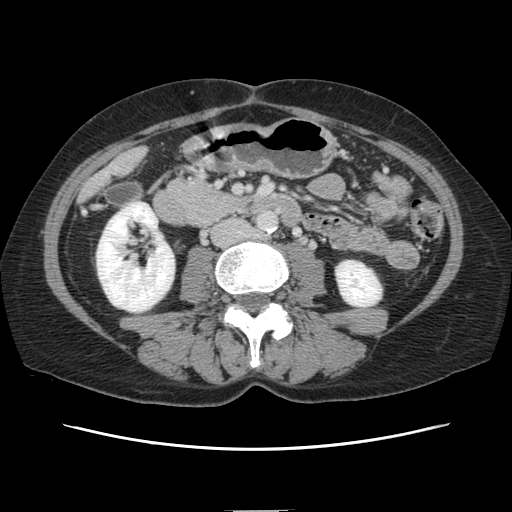
Contrast-enhanced abdominal CT, one axial slice. Slice 27 of 141 in the series (ordered by position). 120 kVp. Intravenous contrast given. Soft-tissue window (W 400 / L 40 HU). 2.5 mm slice thickness. 512 × 512 image matrix. Female patient, age 63 years. From the clinical record (not read from this slice): diagnosis: colorectal cancer liver metastases, imaged before liver resection; multiple liver metastases: yes; largest metastasis: 3.2 cm.
Annotated regions visible in this slice (expert manual segmentation):
- liver: bounding box <84,150,144,197> (left, top, right, bottom; pixels)